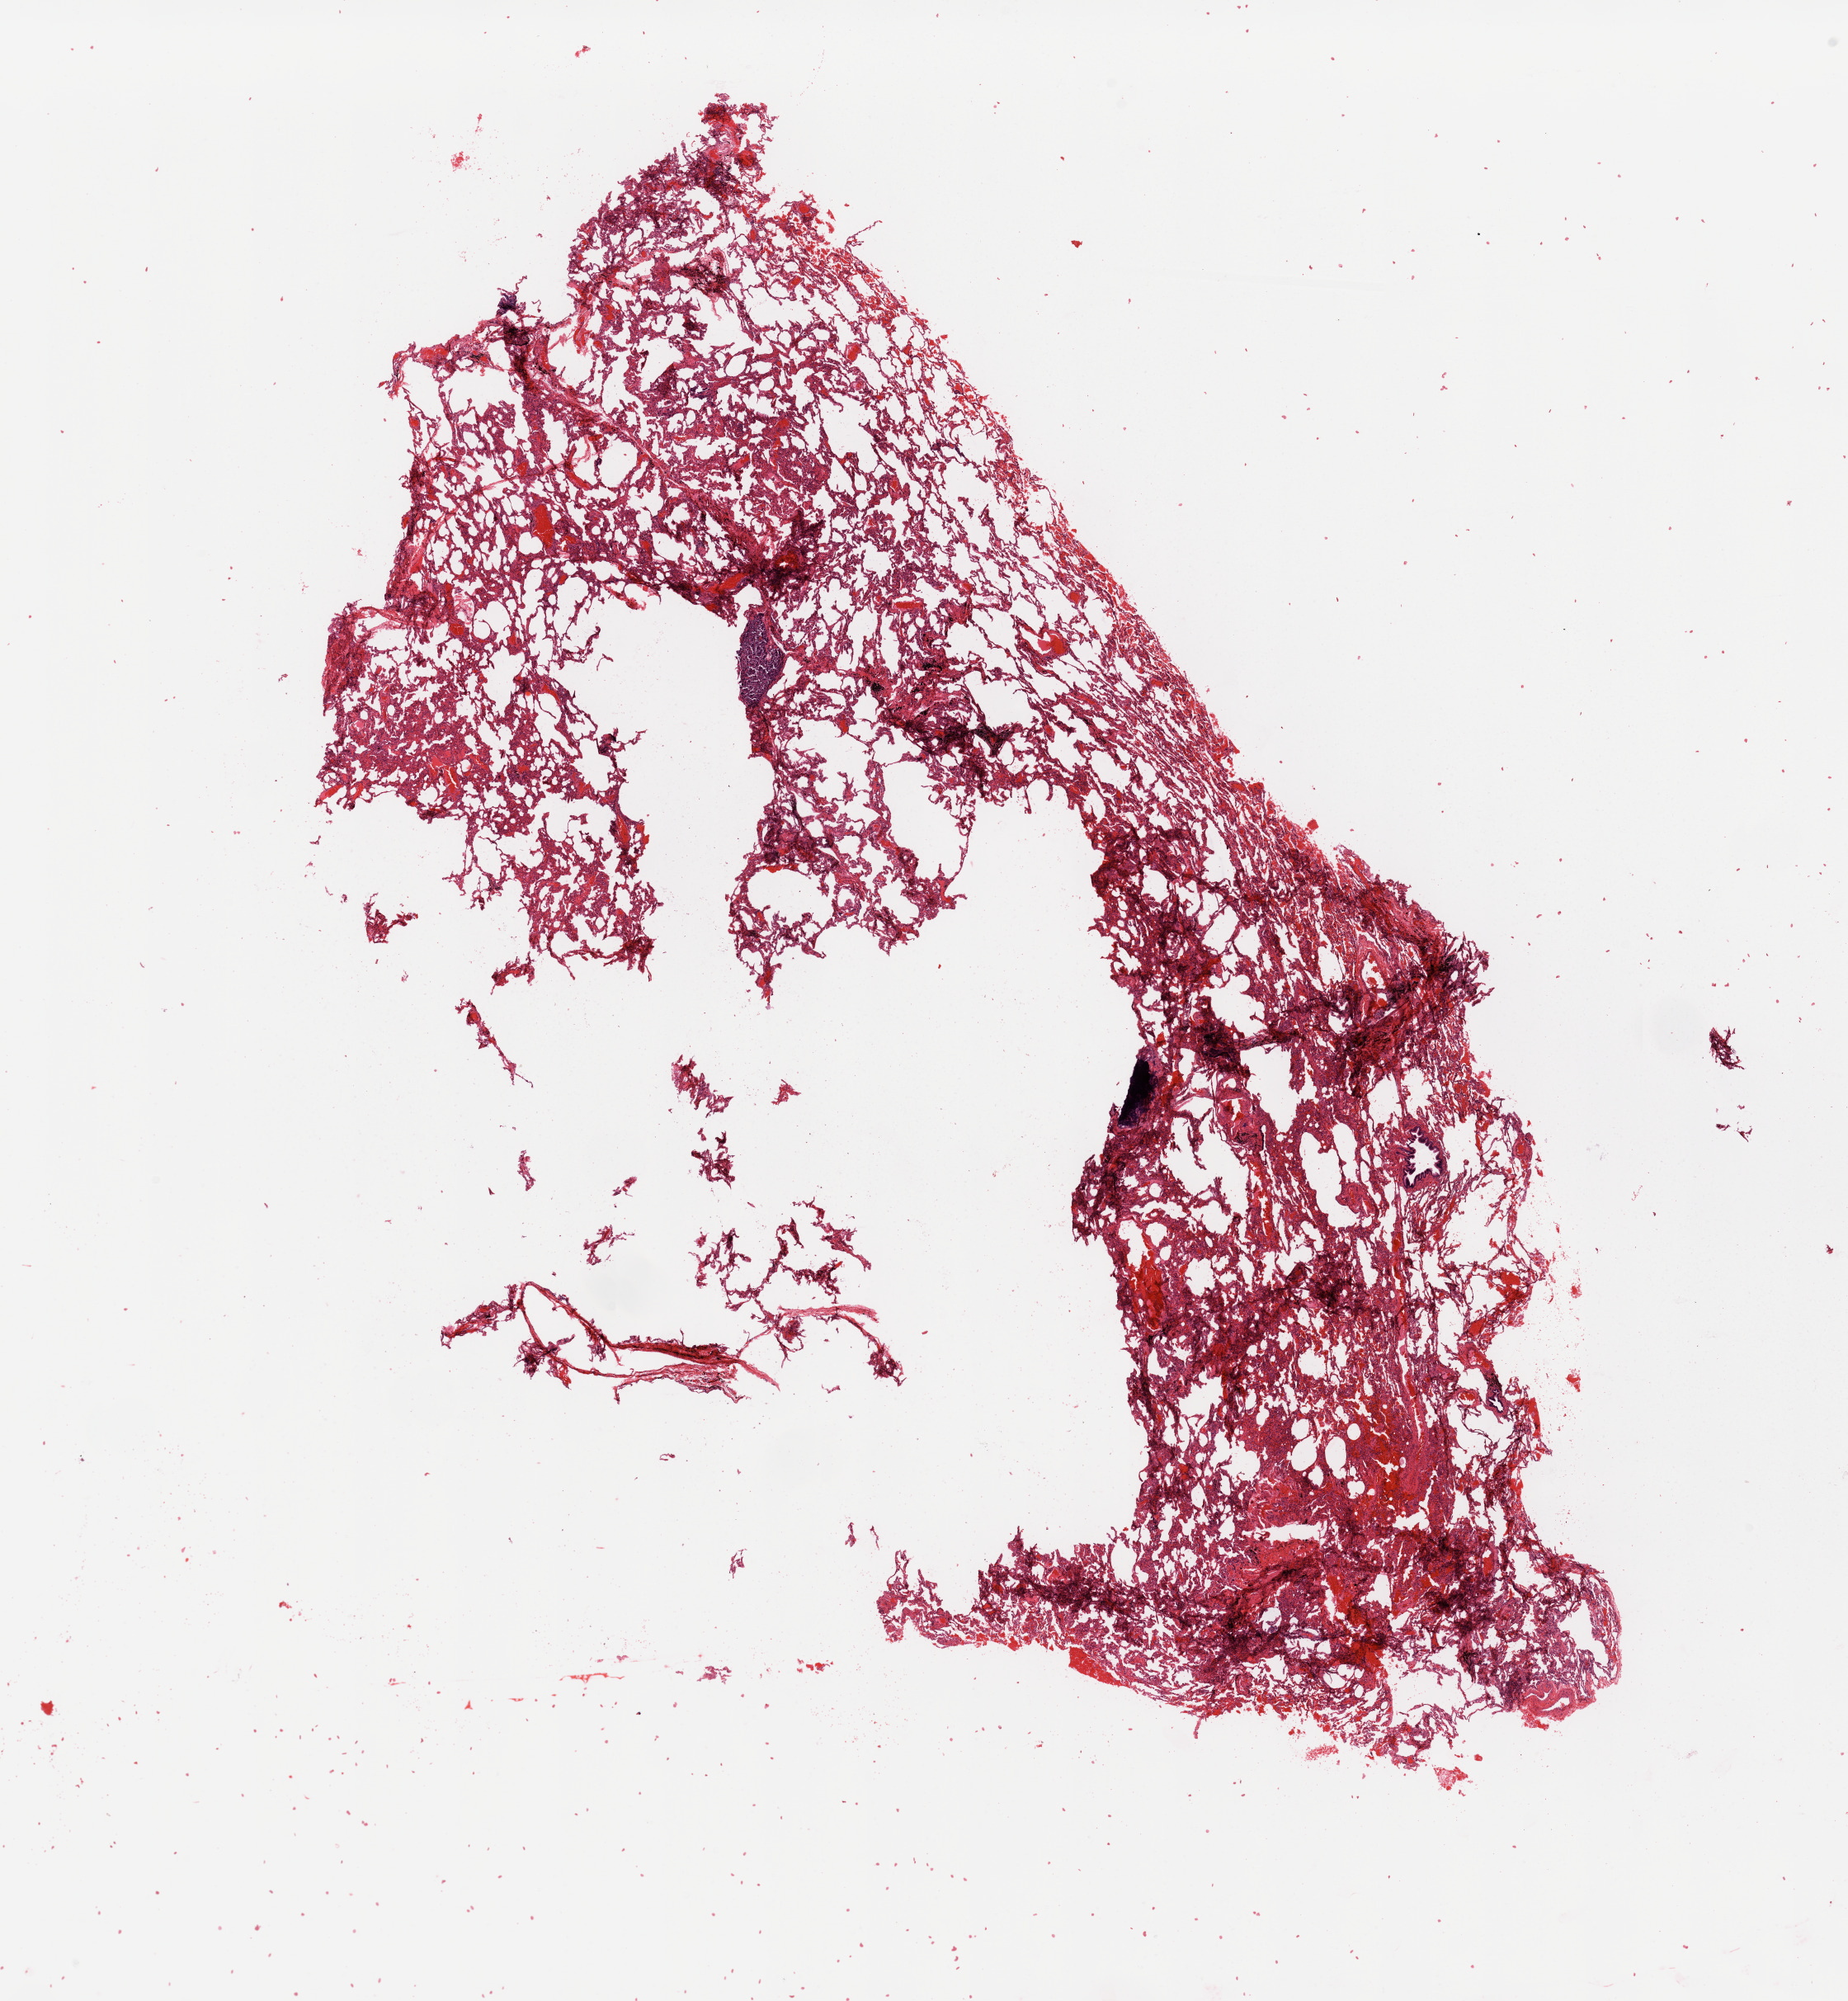
Digitized H&E-stained tissue section (whole slide) — low-resolution overview of the scanned area, about 17.7 x 19.2 mm (slide scanned at 20x); normal (non-tumour) tissue sample, lung. Female, 56 y/o.
• this section: normal (non-tumour) tissue from the same patient
• patient diagnosis: Adenocarcinoma, NOS